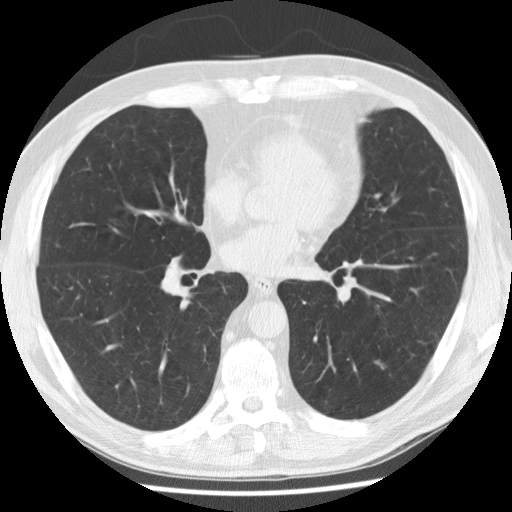
Low-dose screening chest CT, axial slice. Baseline screening round. Lung window (W 1500 / L -600 HU). 2.5 mm slice thickness. 120 kVp. Slice 147 of 265 in the series. 512 × 512 image matrix, field of view 350 × 350 mm. Male, age 58 years at enrolment. Former smoker at enrolment.
Expert-annotated lung lesion, bounding box <368,352,403,384> (left, top, right, bottom; pixels). No non-calcified nodule or mass ≥4 mm was recorded by the screening reader at this exam. Official screen result: negative screen, no significant abnormalities. Lung cancer was diagnosed 798 days after this screen: adenocarcinoma, NOS, left lower lobe, poorly differentiated (G3), stage IA (AJCC 6th edition), 8 mm at pathology.